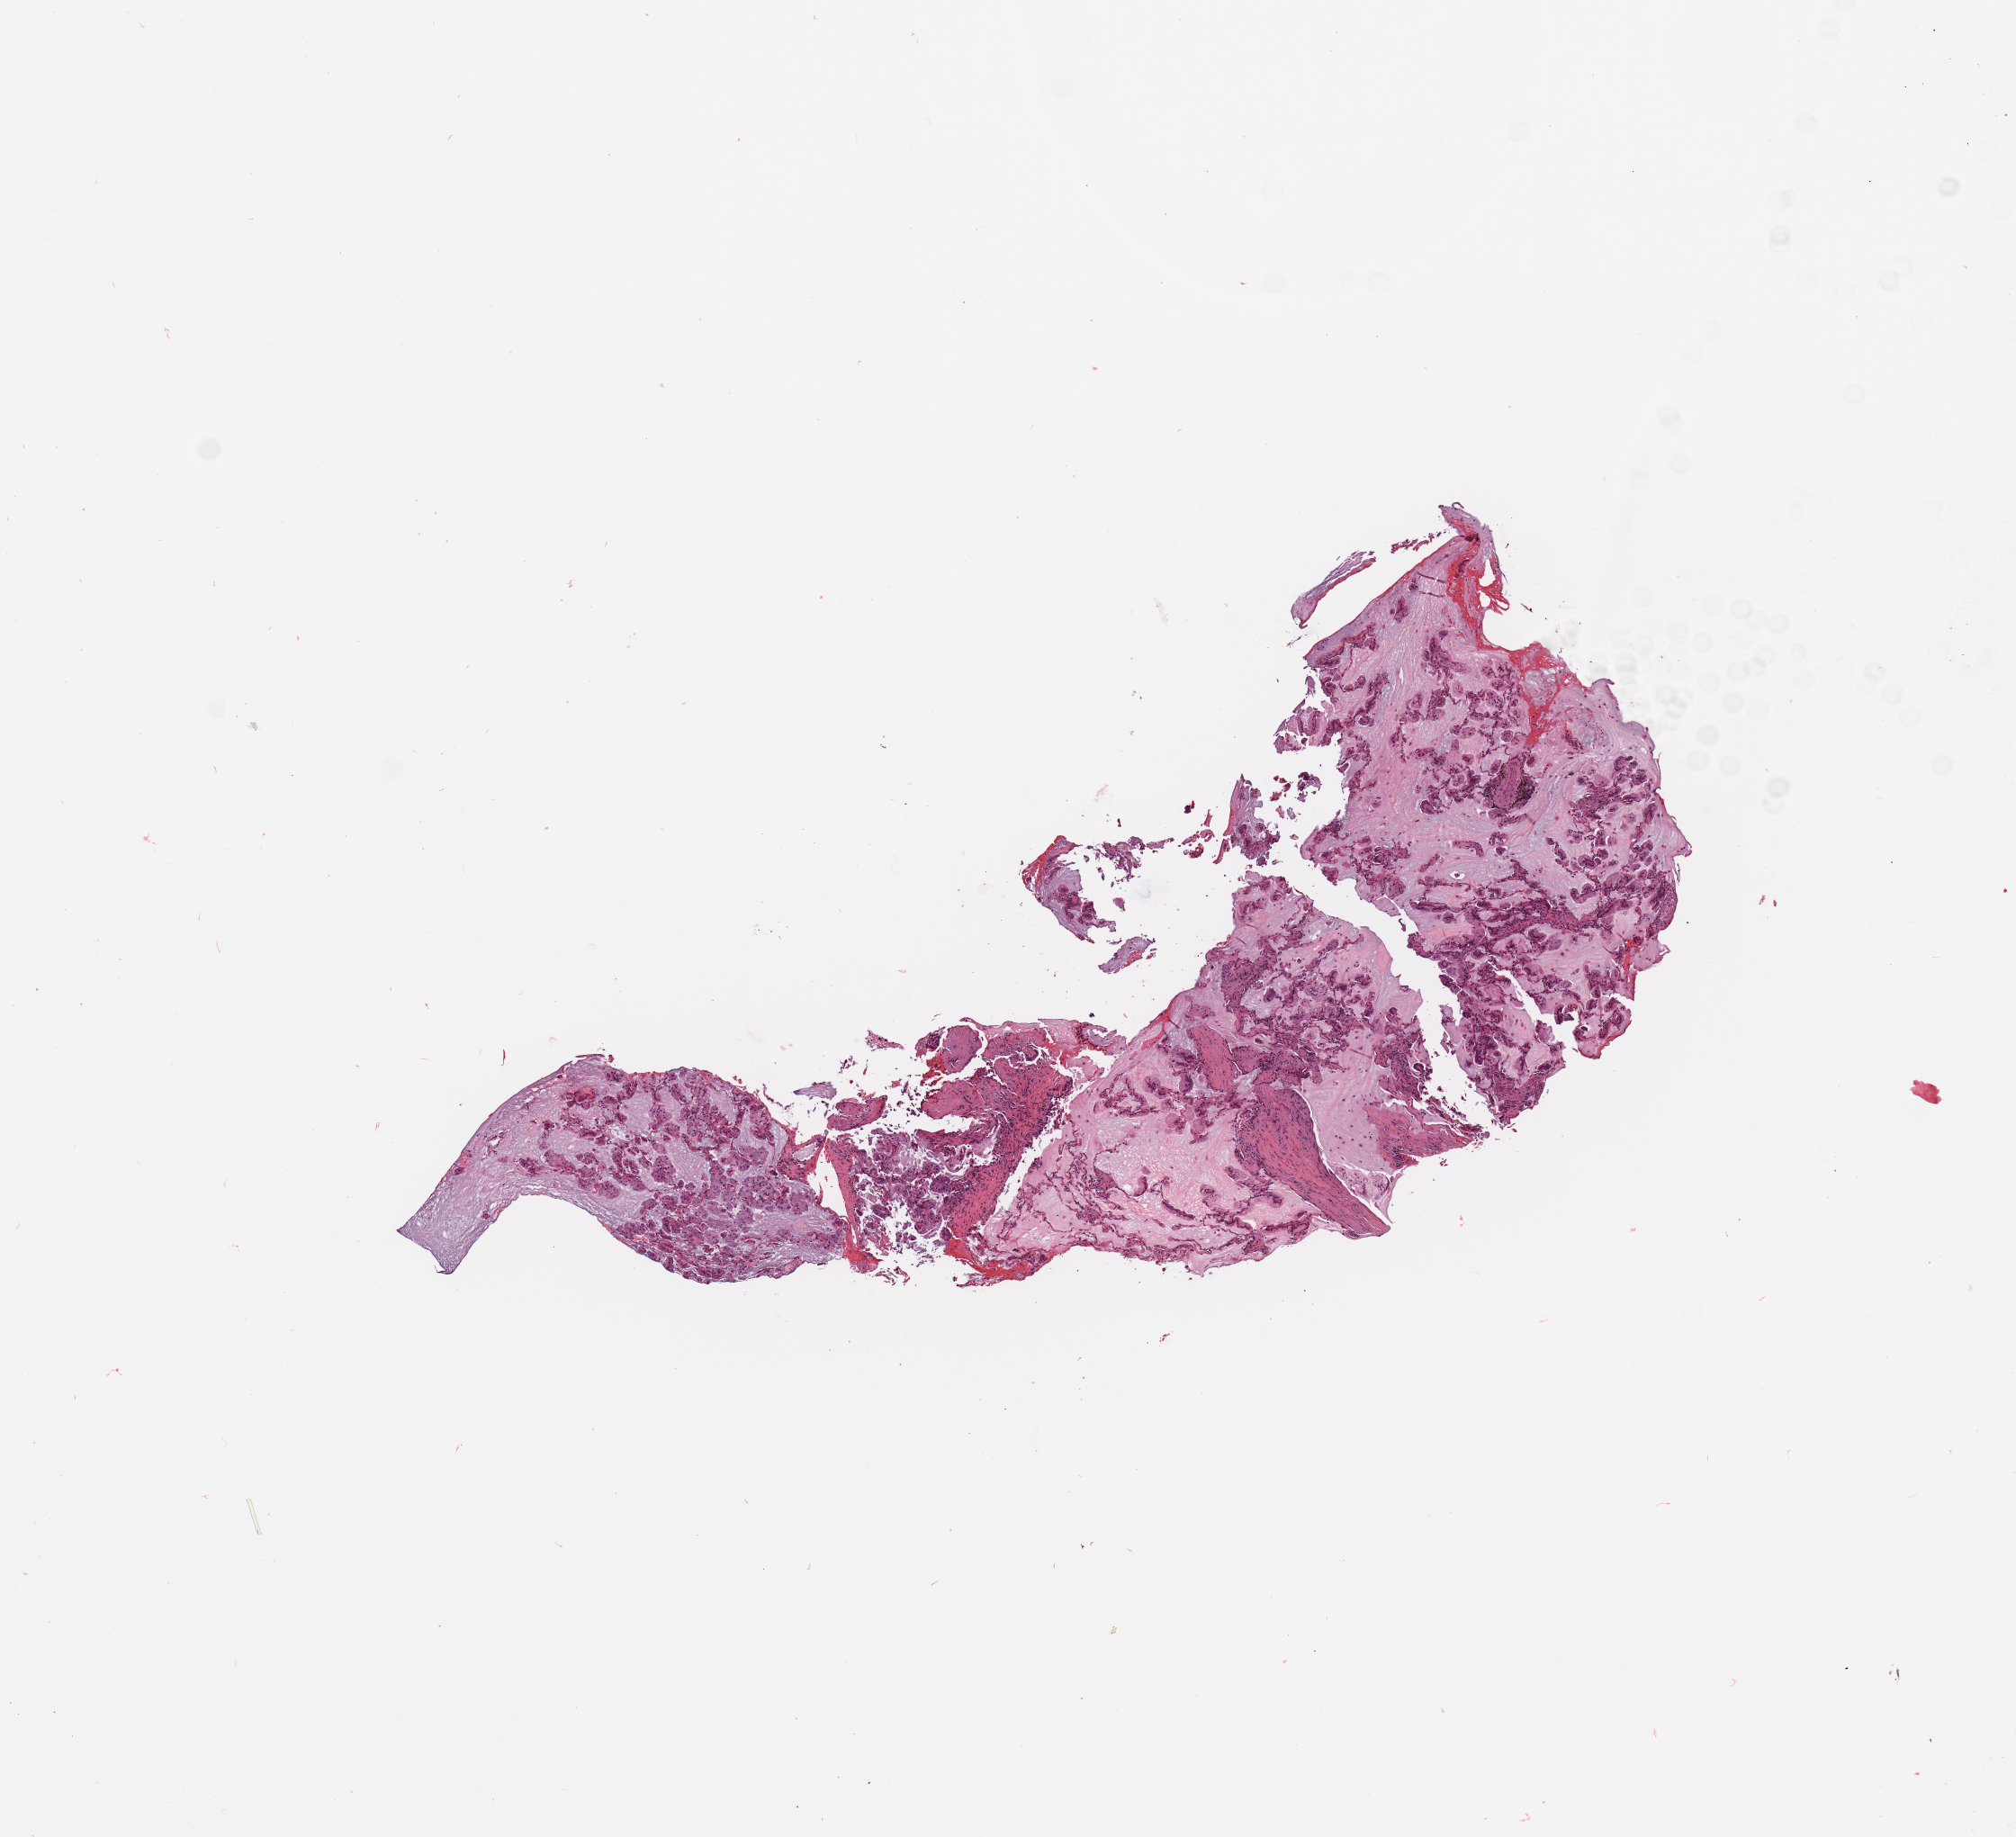
H&E-stained whole-slide image — whole scanned area (about 8.9 x 8.1 mm) shown as a low-resolution overview, lung, tumour tissue. Male, 65 y/o. Histologic grade: G2 (moderately differentiated).
AJCC pathologic stage: IB. Diagnosis: Adenocarcinoma, NOS. Primary tumour site (as recorded): left upper lobe.